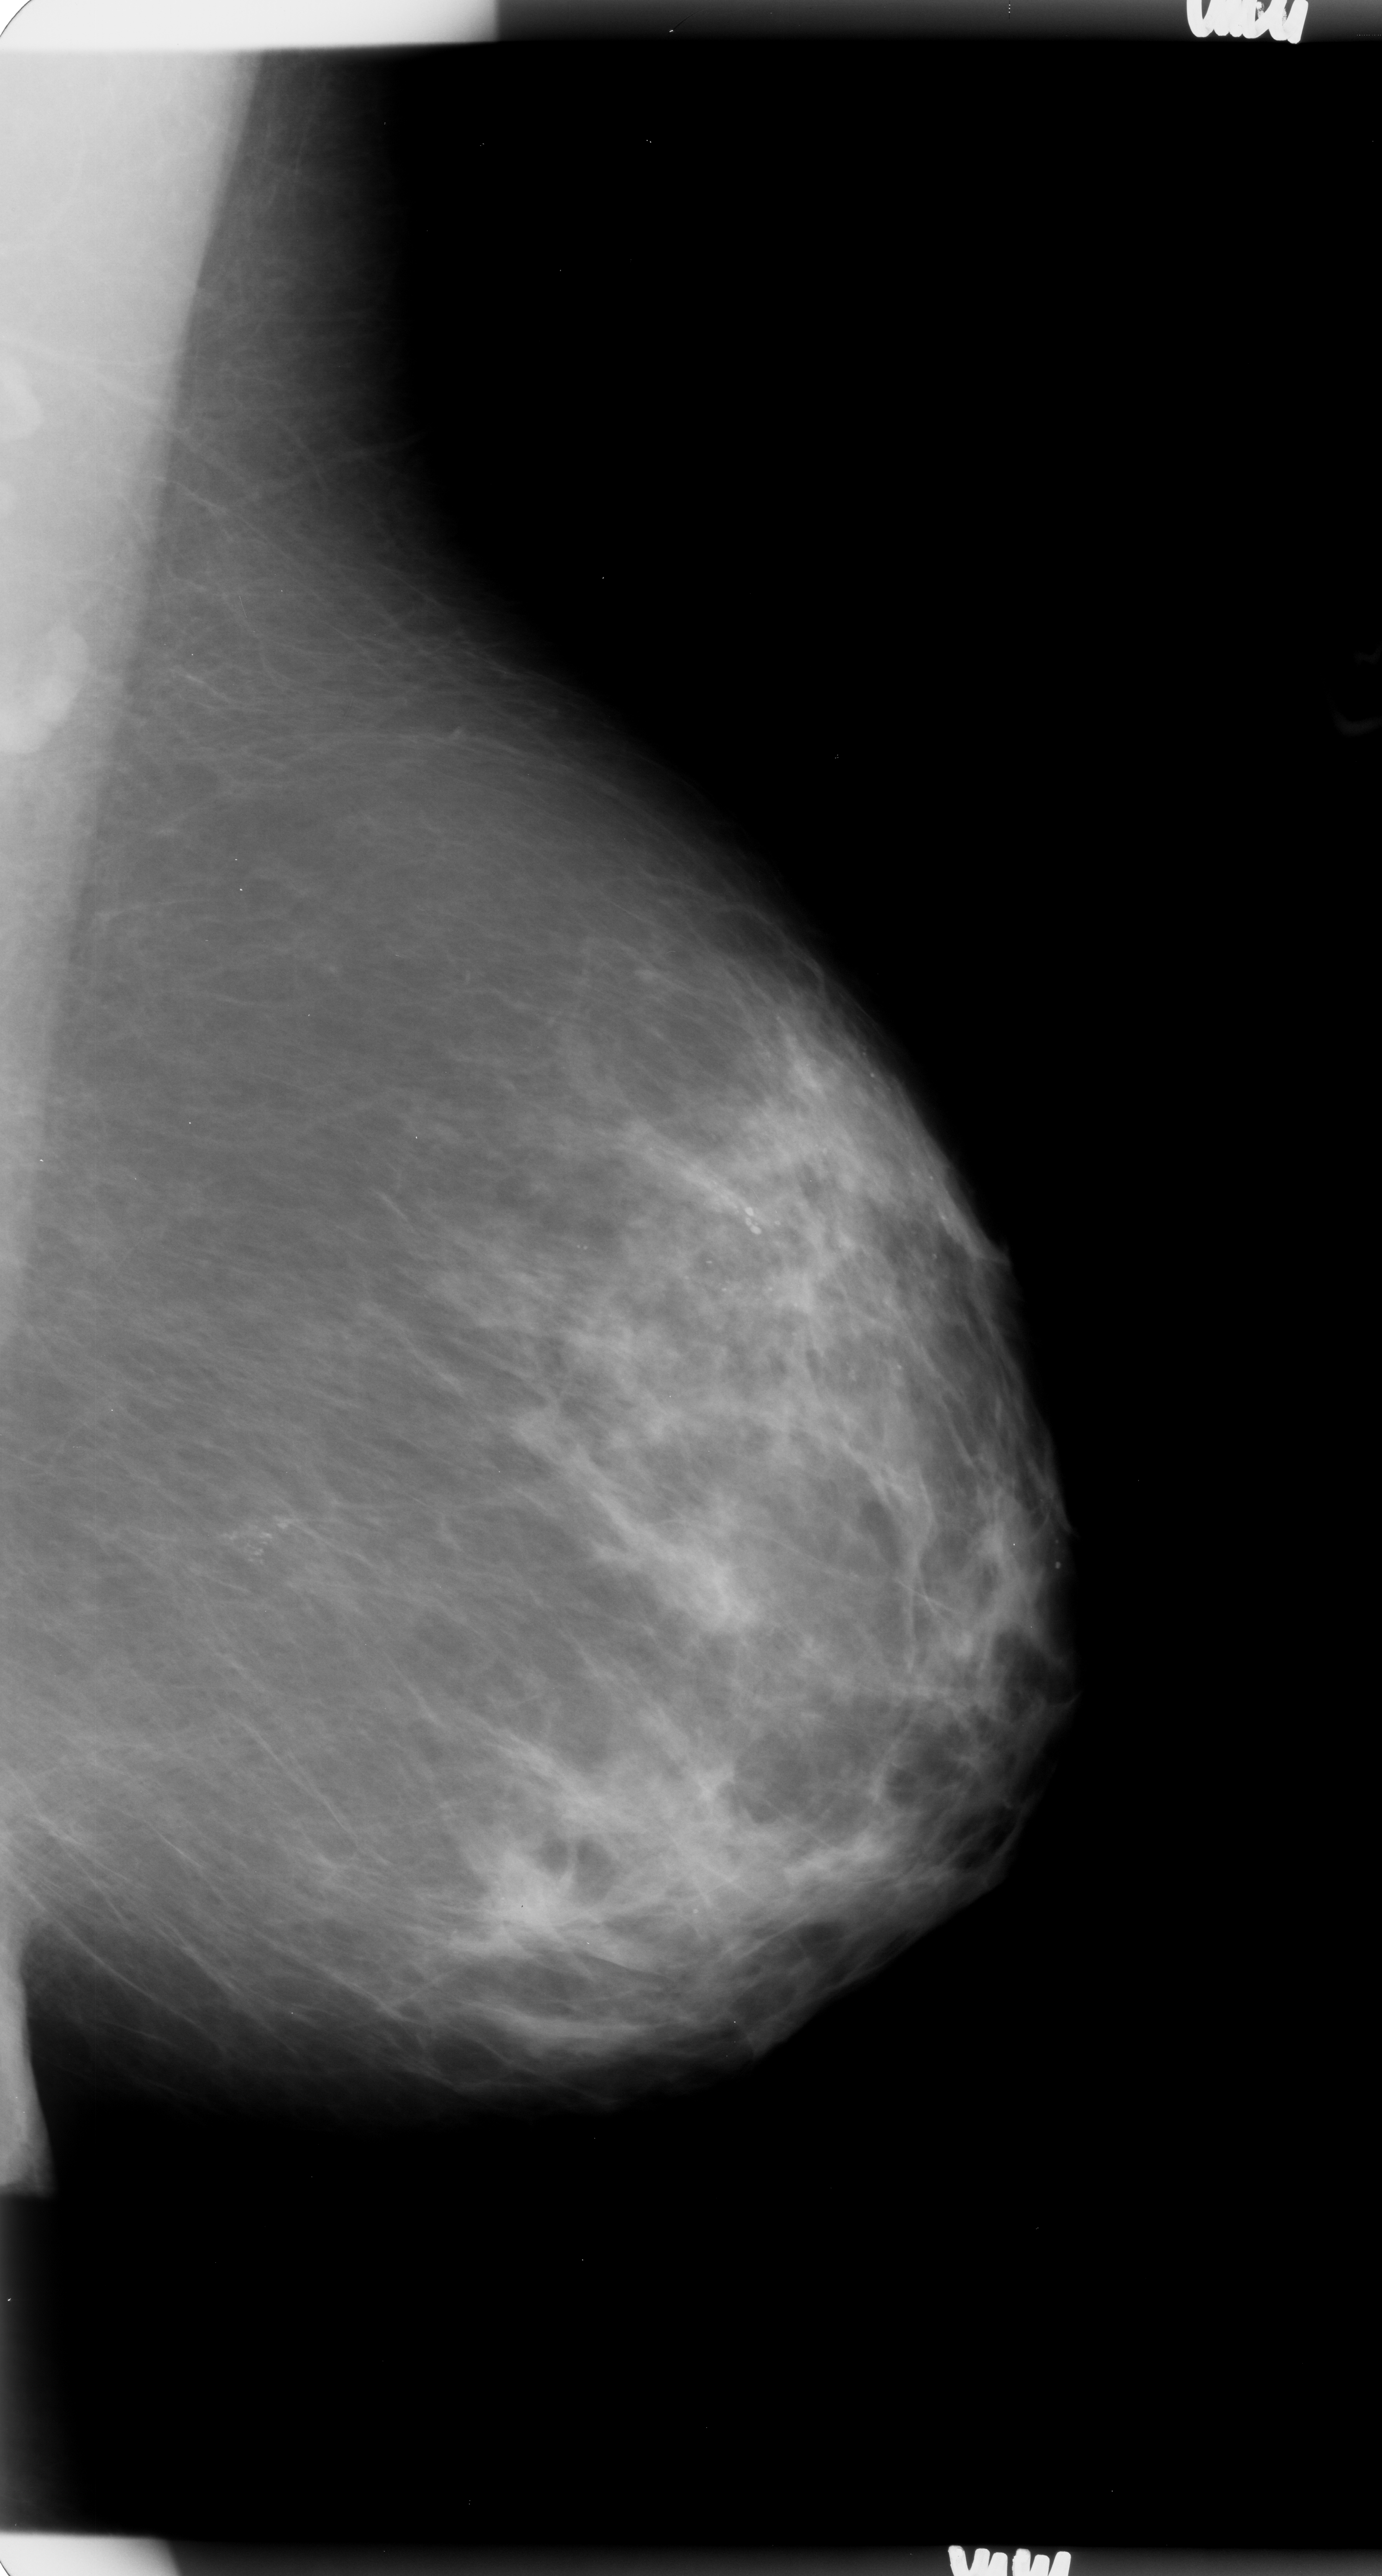
Digitized screen-film mammogram; left breast; mediolateral oblique (MLO) view; breast composition: scattered fibroglandular densities (BI-RADS density category 2 of 4).
Calcifications, morphology pleomorphic, distribution clustered; BI-RADS assessment category 4; pathology result (as recorded, not read from the image): benign.